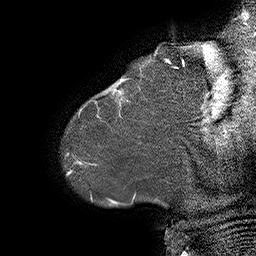
Breast MRI (dynamic contrast-enhanced), one sagittal slice. Position 3 of 55 along the scan axis. Dynamic contrast-enhanced series, time point 2 of 6 at this slice position (early post-contrast). 1.5 T. TE 4.5 ms, TR 32.4 ms. 3 mm slice thickness. 256 × 256 image matrix. Female patient. From the clinical record (not read from this slice): setting: breast cancer imaged before/during neoadjuvant chemotherapy; receptor status: HER2-positive.
Structures marked on this image (semi-automatic segmentation, software-assisted and operator-edited):
- analysis volume of interest (the breast-tissue region the enhancement analysis was run in; not a lesion): bounding box (x1, y1, x2, y2) in pixels: (80, 64, 163, 134)
- tumour enhancement mask (voxels above the 100 % enhancement threshold inside the analysis volume of interest): (97, 79, 125, 117)